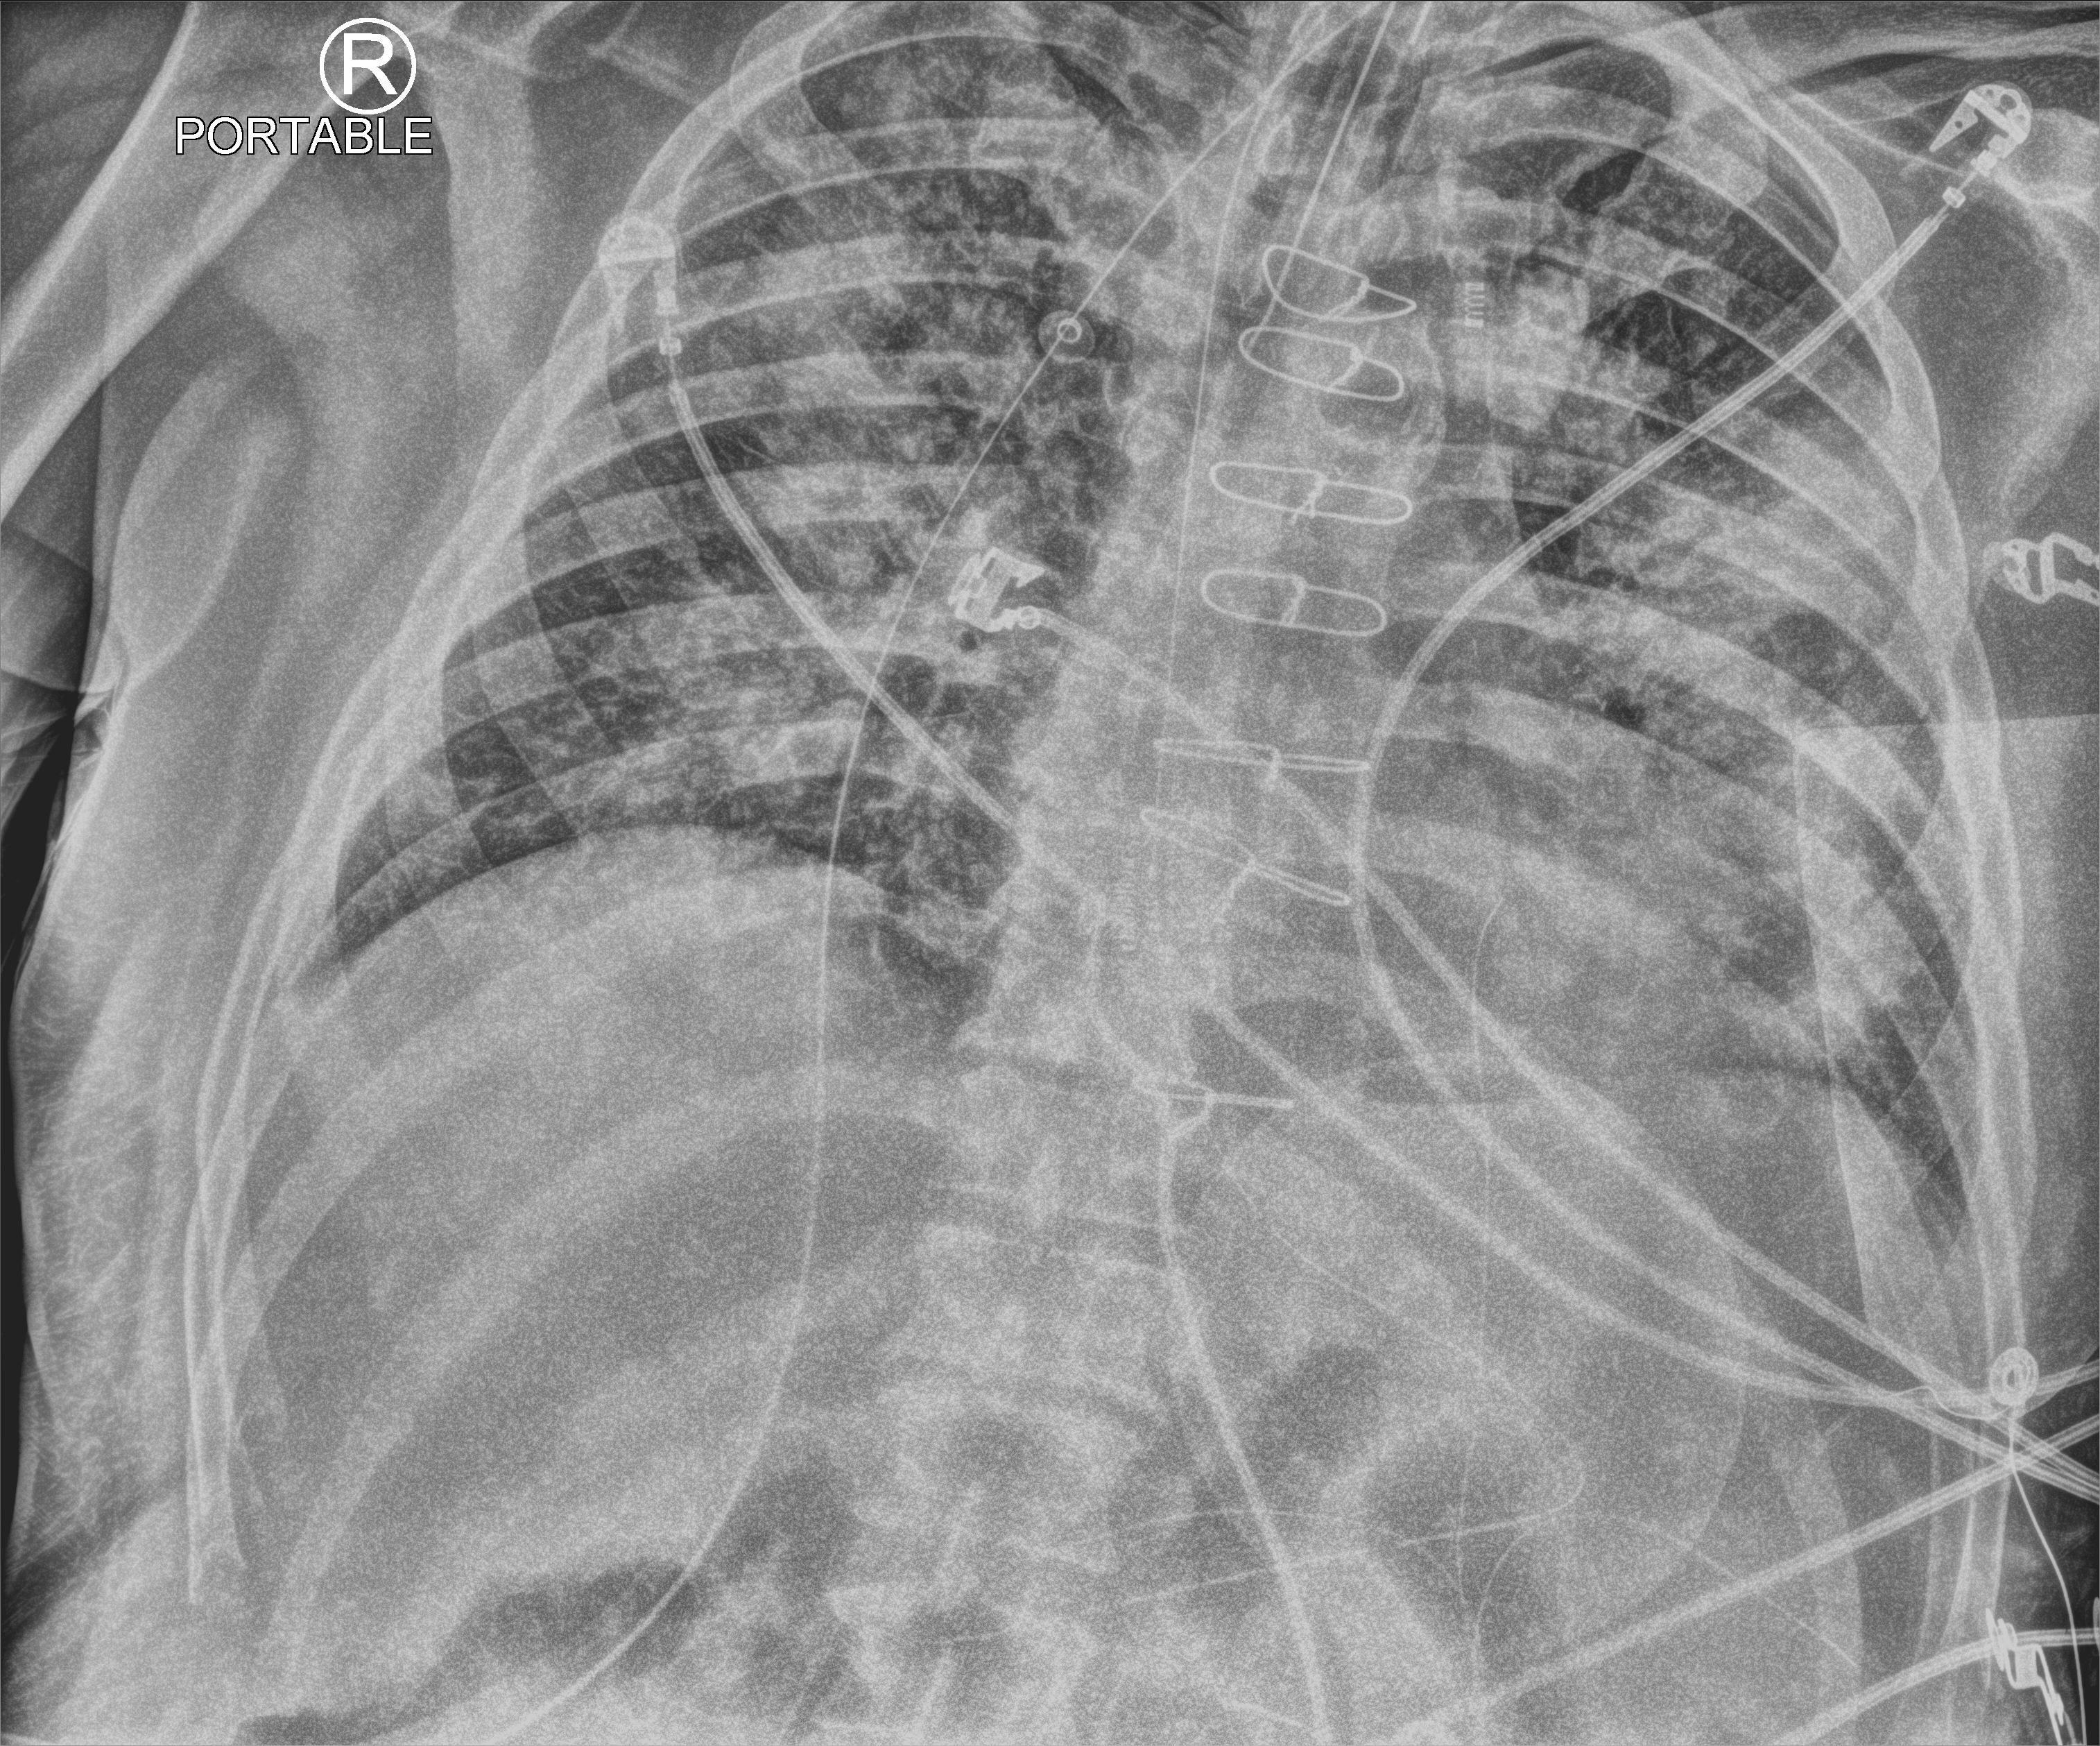
Portable chest radiograph, anteroposterior (AP) projection. Male patient hospitalised with COVID-19, age 60–74 years.
From the hospital-stay record, not from the radiograph (when in the stay this image was taken is not recorded):
- mechanically ventilated during this hospital stay: yes